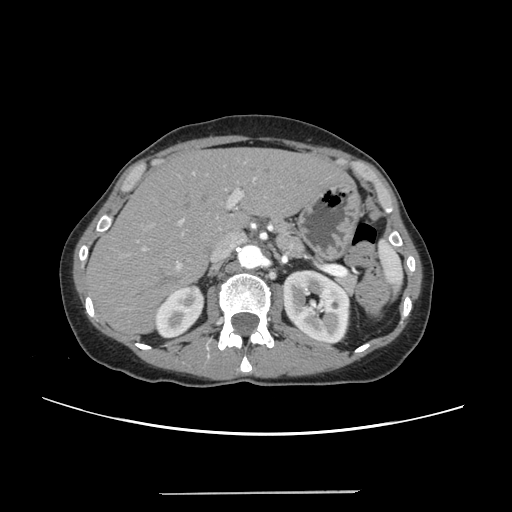
Contrast-enhanced abdominal CT, one axial slice. Position 157 of 240 along the scan axis. 120 kVp. Intravenous contrast given. Soft-tissue window (W 400 / L 40 HU). 1.25 mm slice thickness. 512 × 512 image matrix, field of view 371 × 371 mm. Female patient, age 60 years. Case-level facts recorded for this patient, not image findings: diagnosis: colorectal cancer liver metastases, imaged before liver resection; multiple liver metastases: no; largest metastasis: 1.5 cm; disease in both lobes: no.
Annotated regions visible in this slice (expert manual segmentation):
- liver: box from (x=88, y=149) to (x=347, y=333) px
- planned liver remnant (the part of the liver to remain after resection): (x=88, y=149)–(x=346, y=333)
- portal vein (with intrahepatic branches): (x=143, y=171)–(x=258, y=269)